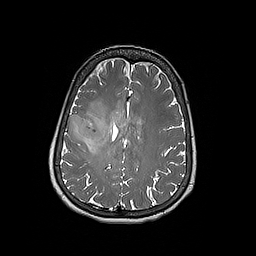
Brain MRI from a brain-tumour surgery series, one axial slice. Slice 75 of 192 in the series (ordered by position). 256 × 256 image matrix, field of view 250 × 250 mm. Case-level facts recorded for this patient, not image findings: histopathology: Oligodendroglioma; WHO grade: 3; IDH mutation: yes; tumour location: Right Frontal.
Structures marked on this image (manually delineated by an expert):
- tumour: box from (x=67, y=114) to (x=108, y=150) px